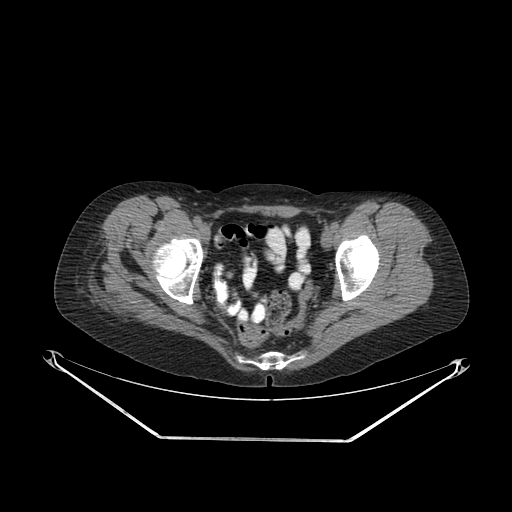
CT of an extremity soft-tissue mass (from a PET/CT study), one axial slice; position 55 of 267 along the scan axis; reconstruction kernel SOFT; 140 kVp; soft-tissue window (W 400 / L 40 HU); 3.75 mm slice thickness; 512 × 512 image matrix. Female patient. Case-level facts recorded for this patient, not image findings: histological type: epithelioid sarcoma with vascular differentiation; site of the primary tumour: right buttock.
Outlined on this slice (expert contour drawn on MRI and transferred to this co-registered scan by the dataset authors):
- gross tumour volume (mass): bounding box [x1, y1, x2, y2] px = [78, 271, 131, 312]